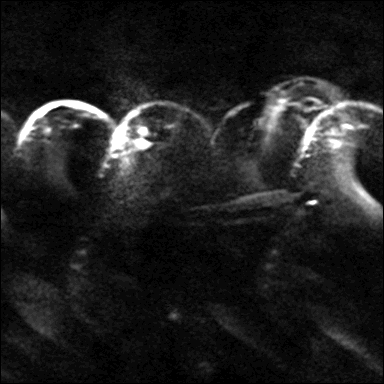
Breast MRI, one axial slice. Position 25 of 36 along the scan axis. Diffusion-weighted series; image 2 of 4 stored at this slice position (different b-values; order by instance number). 3 T. 4 mm slice thickness. 384 × 384 image matrix, field of view 320 × 320 mm. Female patient.
Annotated regions visible in this slice (expert manual segmentation):
- tumour on diffusion-weighted imaging: box from (x=46, y=129) to (x=50, y=133) px